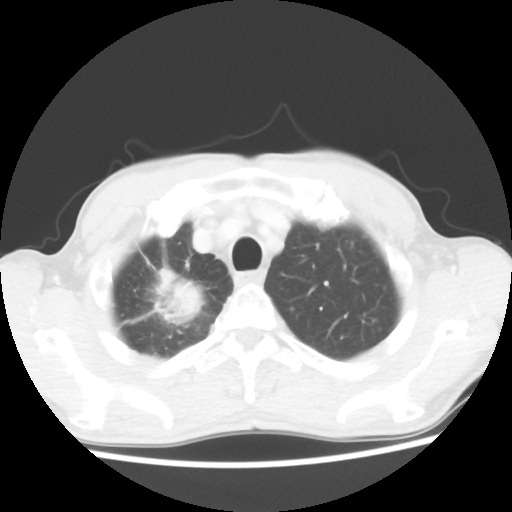
Chest CT, one axial slice; slice 45 of 52 in the series (ordered by position); reconstruction kernel STANDARD; 100 kVp; lung window (W 1500 / L -600 HU); 5 mm slice thickness; 512 × 512 image matrix, field of view 323 × 323 mm. Male patient, age 66 years. From the clinical record (not read from this slice): clinical TNM (as recorded): T2 N0 M1a.
Annotated regions visible in this slice (rectangle marked by the reading radiologist):
- lung tumour (recorded histology: adenocarcinoma): bounding box <140,265,208,328> (left, top, right, bottom; pixels)